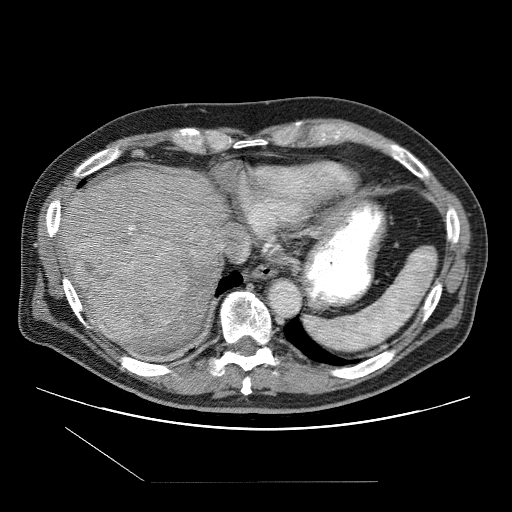
Contrast-enhanced abdominal CT (liver protocol), one axial slice. Slice 86 of 109 in the series (ordered by position). One of 2 acquisitions stored at this slice position. Soft-tissue window (W 400 / L 40 HU). 2.5 mm slice thickness. 512 × 512 image matrix. Case-level facts recorded for this patient, not image findings: diagnosis: hepatocellular carcinoma (patient treated with transarterial chemoembolisation; whether this scan precedes or follows treatment is not stated here); TNM stage (as recorded): Stage-IIIB.
Outlined on this slice (semi-automatic segmentation, software-assisted and operator-edited):
- liver parenchyma outside the tumour (the mass and vessels are separate outlines, so this box may not span the whole liver): bounding box [x1, y1, x2, y2] px = [61, 168, 304, 346]
- mass: [70, 233, 191, 341]
- liver vessels: [101, 202, 297, 328]